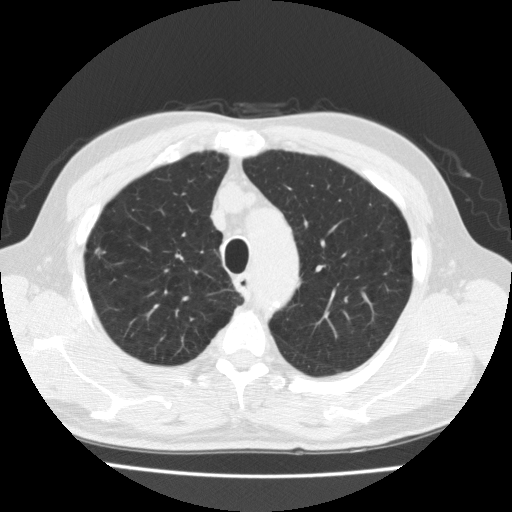
Low-dose screening chest CT, one axial slice; position 167 of 205 along the scan axis; reconstruction kernel FC10; 120 kVp; lung window (W 1500 / L -600 HU); 2 mm slice thickness; 512 × 512 image matrix, field of view 350 × 350 mm.
Annotated regions visible in this slice (expert manual segmentation):
- lesion 1 (tumor, upper lobe of right lung): bounding box [x1, y1, x2, y2] px = [94, 247, 106, 256]